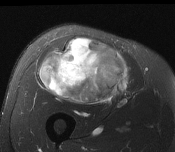
MRI of an extremity soft-tissue mass, one axial slice; slice 85 of 116 in the series (ordered by position); T2-weighted fat-saturated; MR volume resampled by the dataset authors to the PET/CT grid (not the native acquisition matrix); 3.27 mm slice thickness; 175 × 152 image matrix. Male patient. From the clinical record (not read from this slice): histological type: pleiomorphic leiomyosarcoma; grade: intermediate; site of the primary tumour: right thigh.
Annotated regions visible in this slice (expert contour drawn on MRI and transferred to this co-registered scan by the dataset authors):
- gross tumour volume including surrounding oedema: box from (x=40, y=38) to (x=130, y=105) px
- gross tumour volume (mass): (x=40, y=38)–(x=130, y=105)